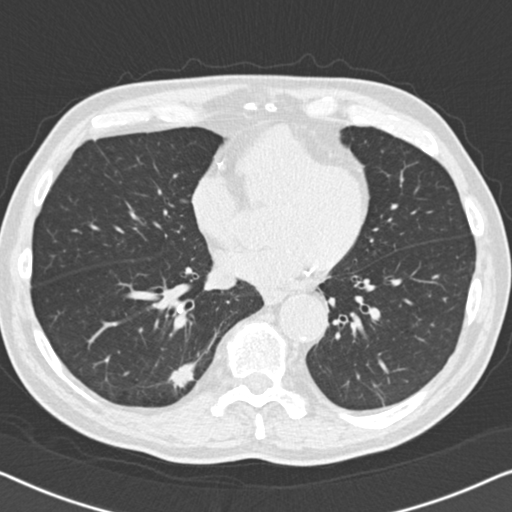
Axial slice from a low-dose chest CT screening exam; second screening round (one year after baseline); lung window (W 1500 / L -600 HU); 2 mm slice thickness. Male, age 74 years at enrolment. Current smoker at enrolment.
Lesion marked by an expert reader, box from (x=148, y=342) to (x=218, y=408) px. The screening reader recorded 5 non-calcified nodules or masses ≥4 mm on this exam (right lower lobe, right lower lobe, right lower lobe, left lower lobe, left lower lobe); which of them this box marks is not recorded. Later outcome: lung cancer diagnosed 55 days after this screen — bronchiolo-alveolar adenocarcinoma, NOS, right lower lobe, moderately differentiated (G2), stage IA (AJCC 6th edition), 16 mm at pathology.